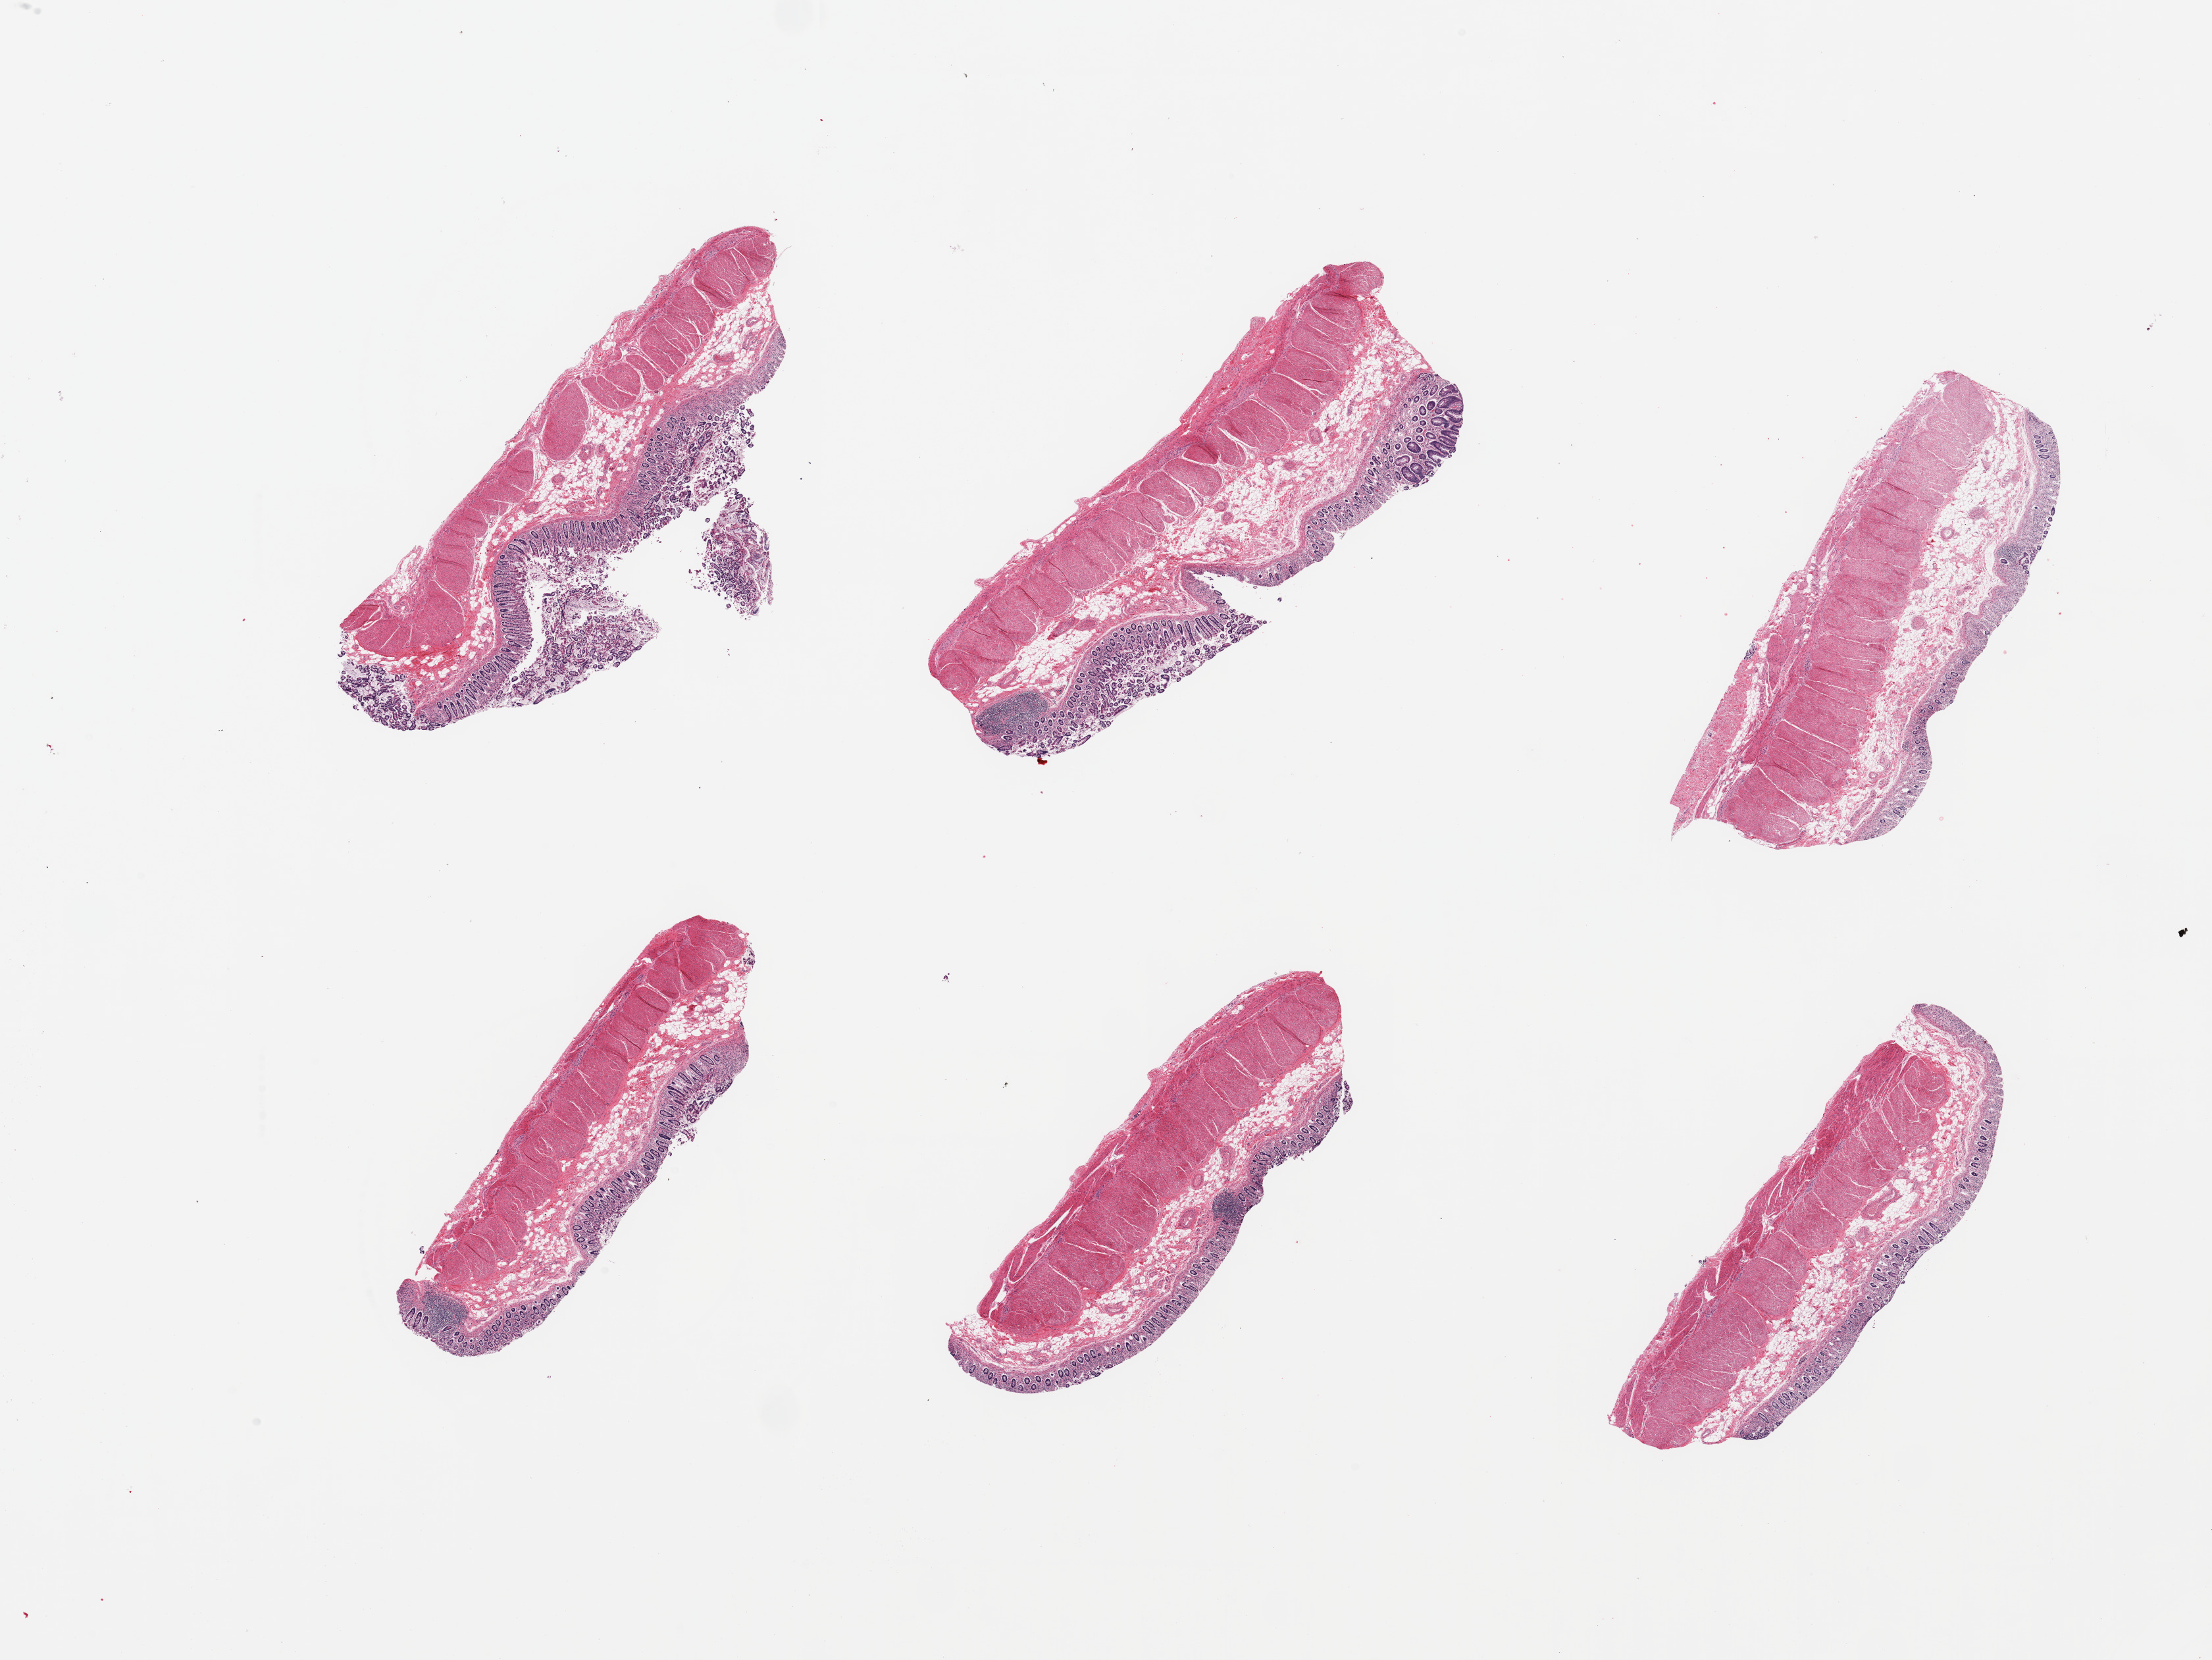
Whole-slide image, haematoxylin and eosin stain, whole scanned area (about 26.6 x 19.9 mm) shown as a low-resolution overview; PAXgene-fixed, paraffin-embedded tissue; sampled site (target tissue): transverse colon; tissue donor sample. Female donor.
- pathologist's review note for this sample: 6 pieces; mucosa largely autolyzed; muscularis intact